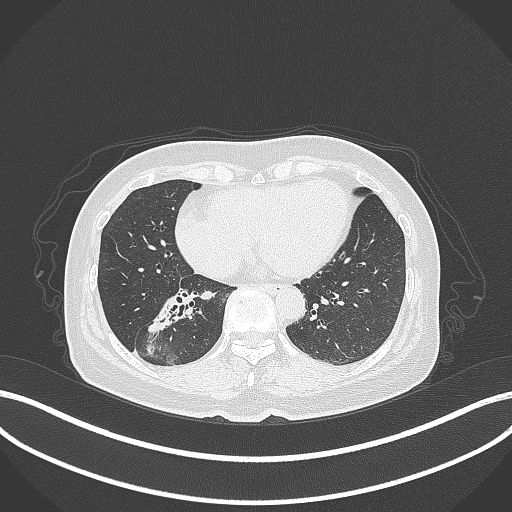
Chest CT, one axial slice. Position 144 of 429 along the scan axis. Reconstruction kernel B70f. 120 kVp. Lung window (W 1500 / L -600 HU). 512 × 512 image matrix, field of view 400 × 400 mm. Female patient, age 67 years. Case-level facts recorded for this patient, not image findings: clinical TNM (as recorded): T1c N1 M0; histopathological grade: G2-3.
Outlined on this slice (rectangle marked by the reading radiologist):
- lung tumour (recorded histology: adenocarcinoma): bounding box (x1, y1, x2, y2) in pixels: (150, 290, 201, 336)